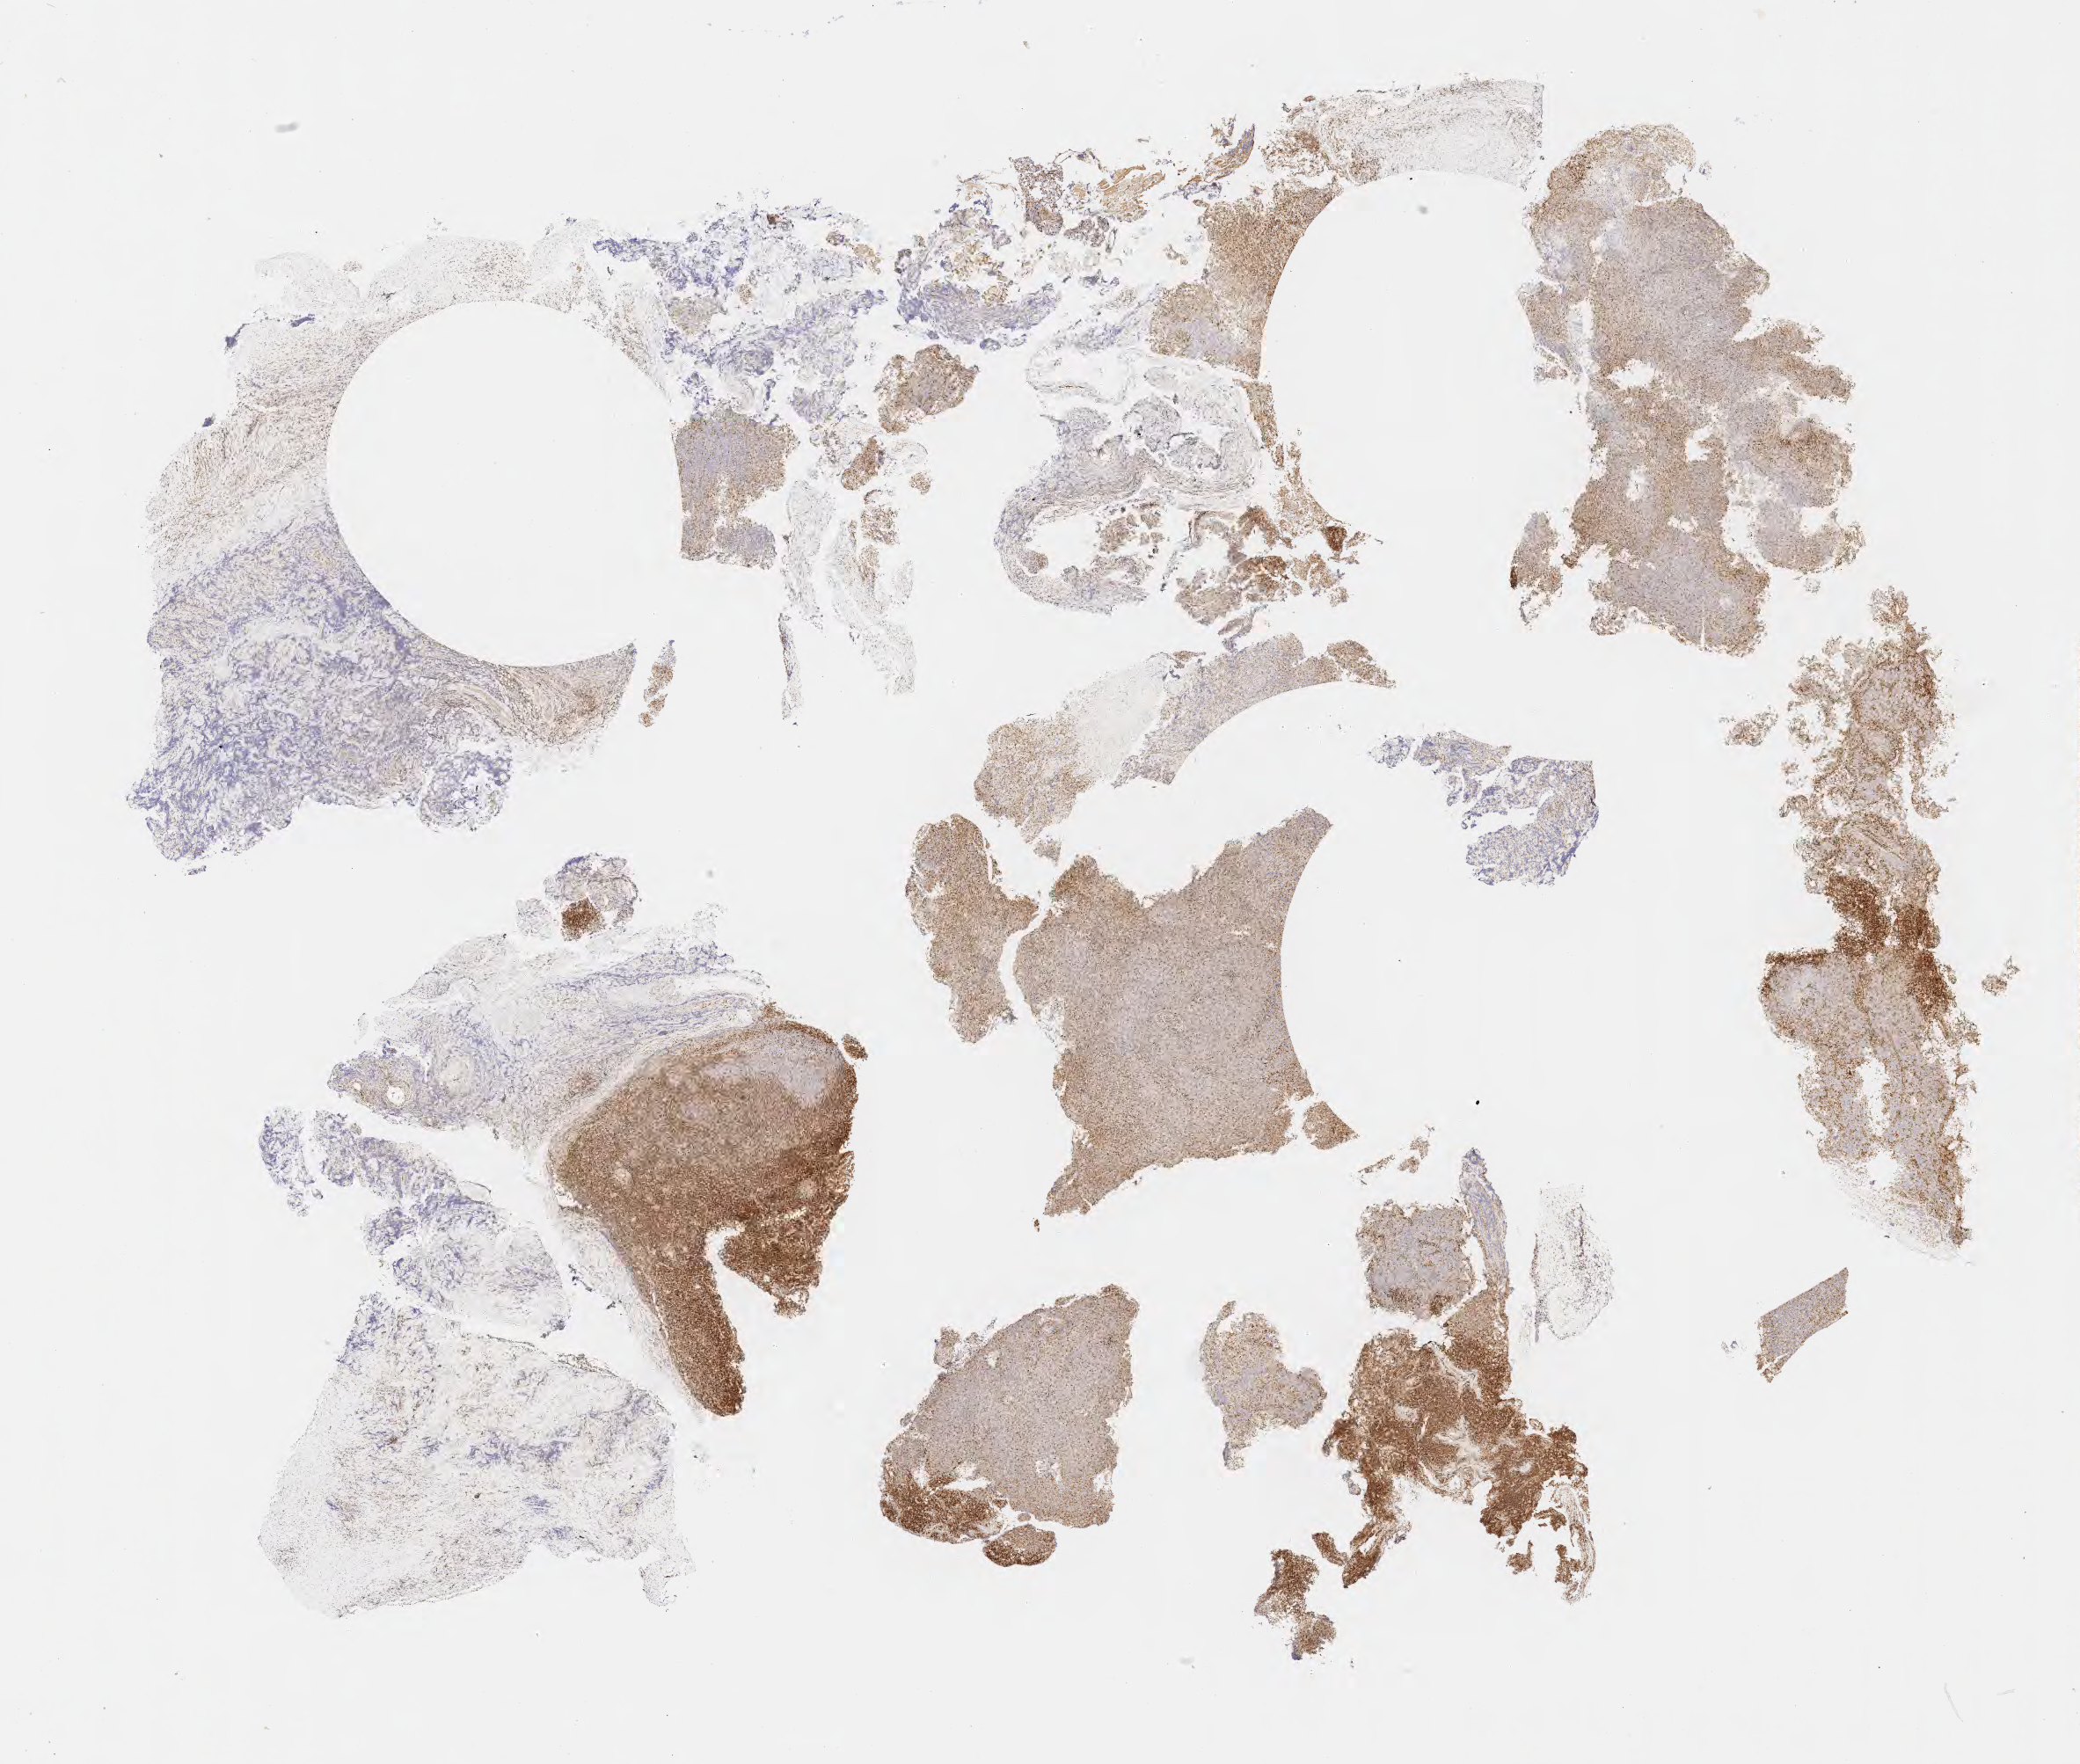
Whole-slide image, immunohistochemical stain for BCL2, a low-resolution overview of the entire scanned area, about 19.1 x 16.2 mm. Tumor tissue. Anatomic site: lymph node. Patient male; age 29 years.
Diagnosis: Diffuse large B-cell lymphoma, NOS.